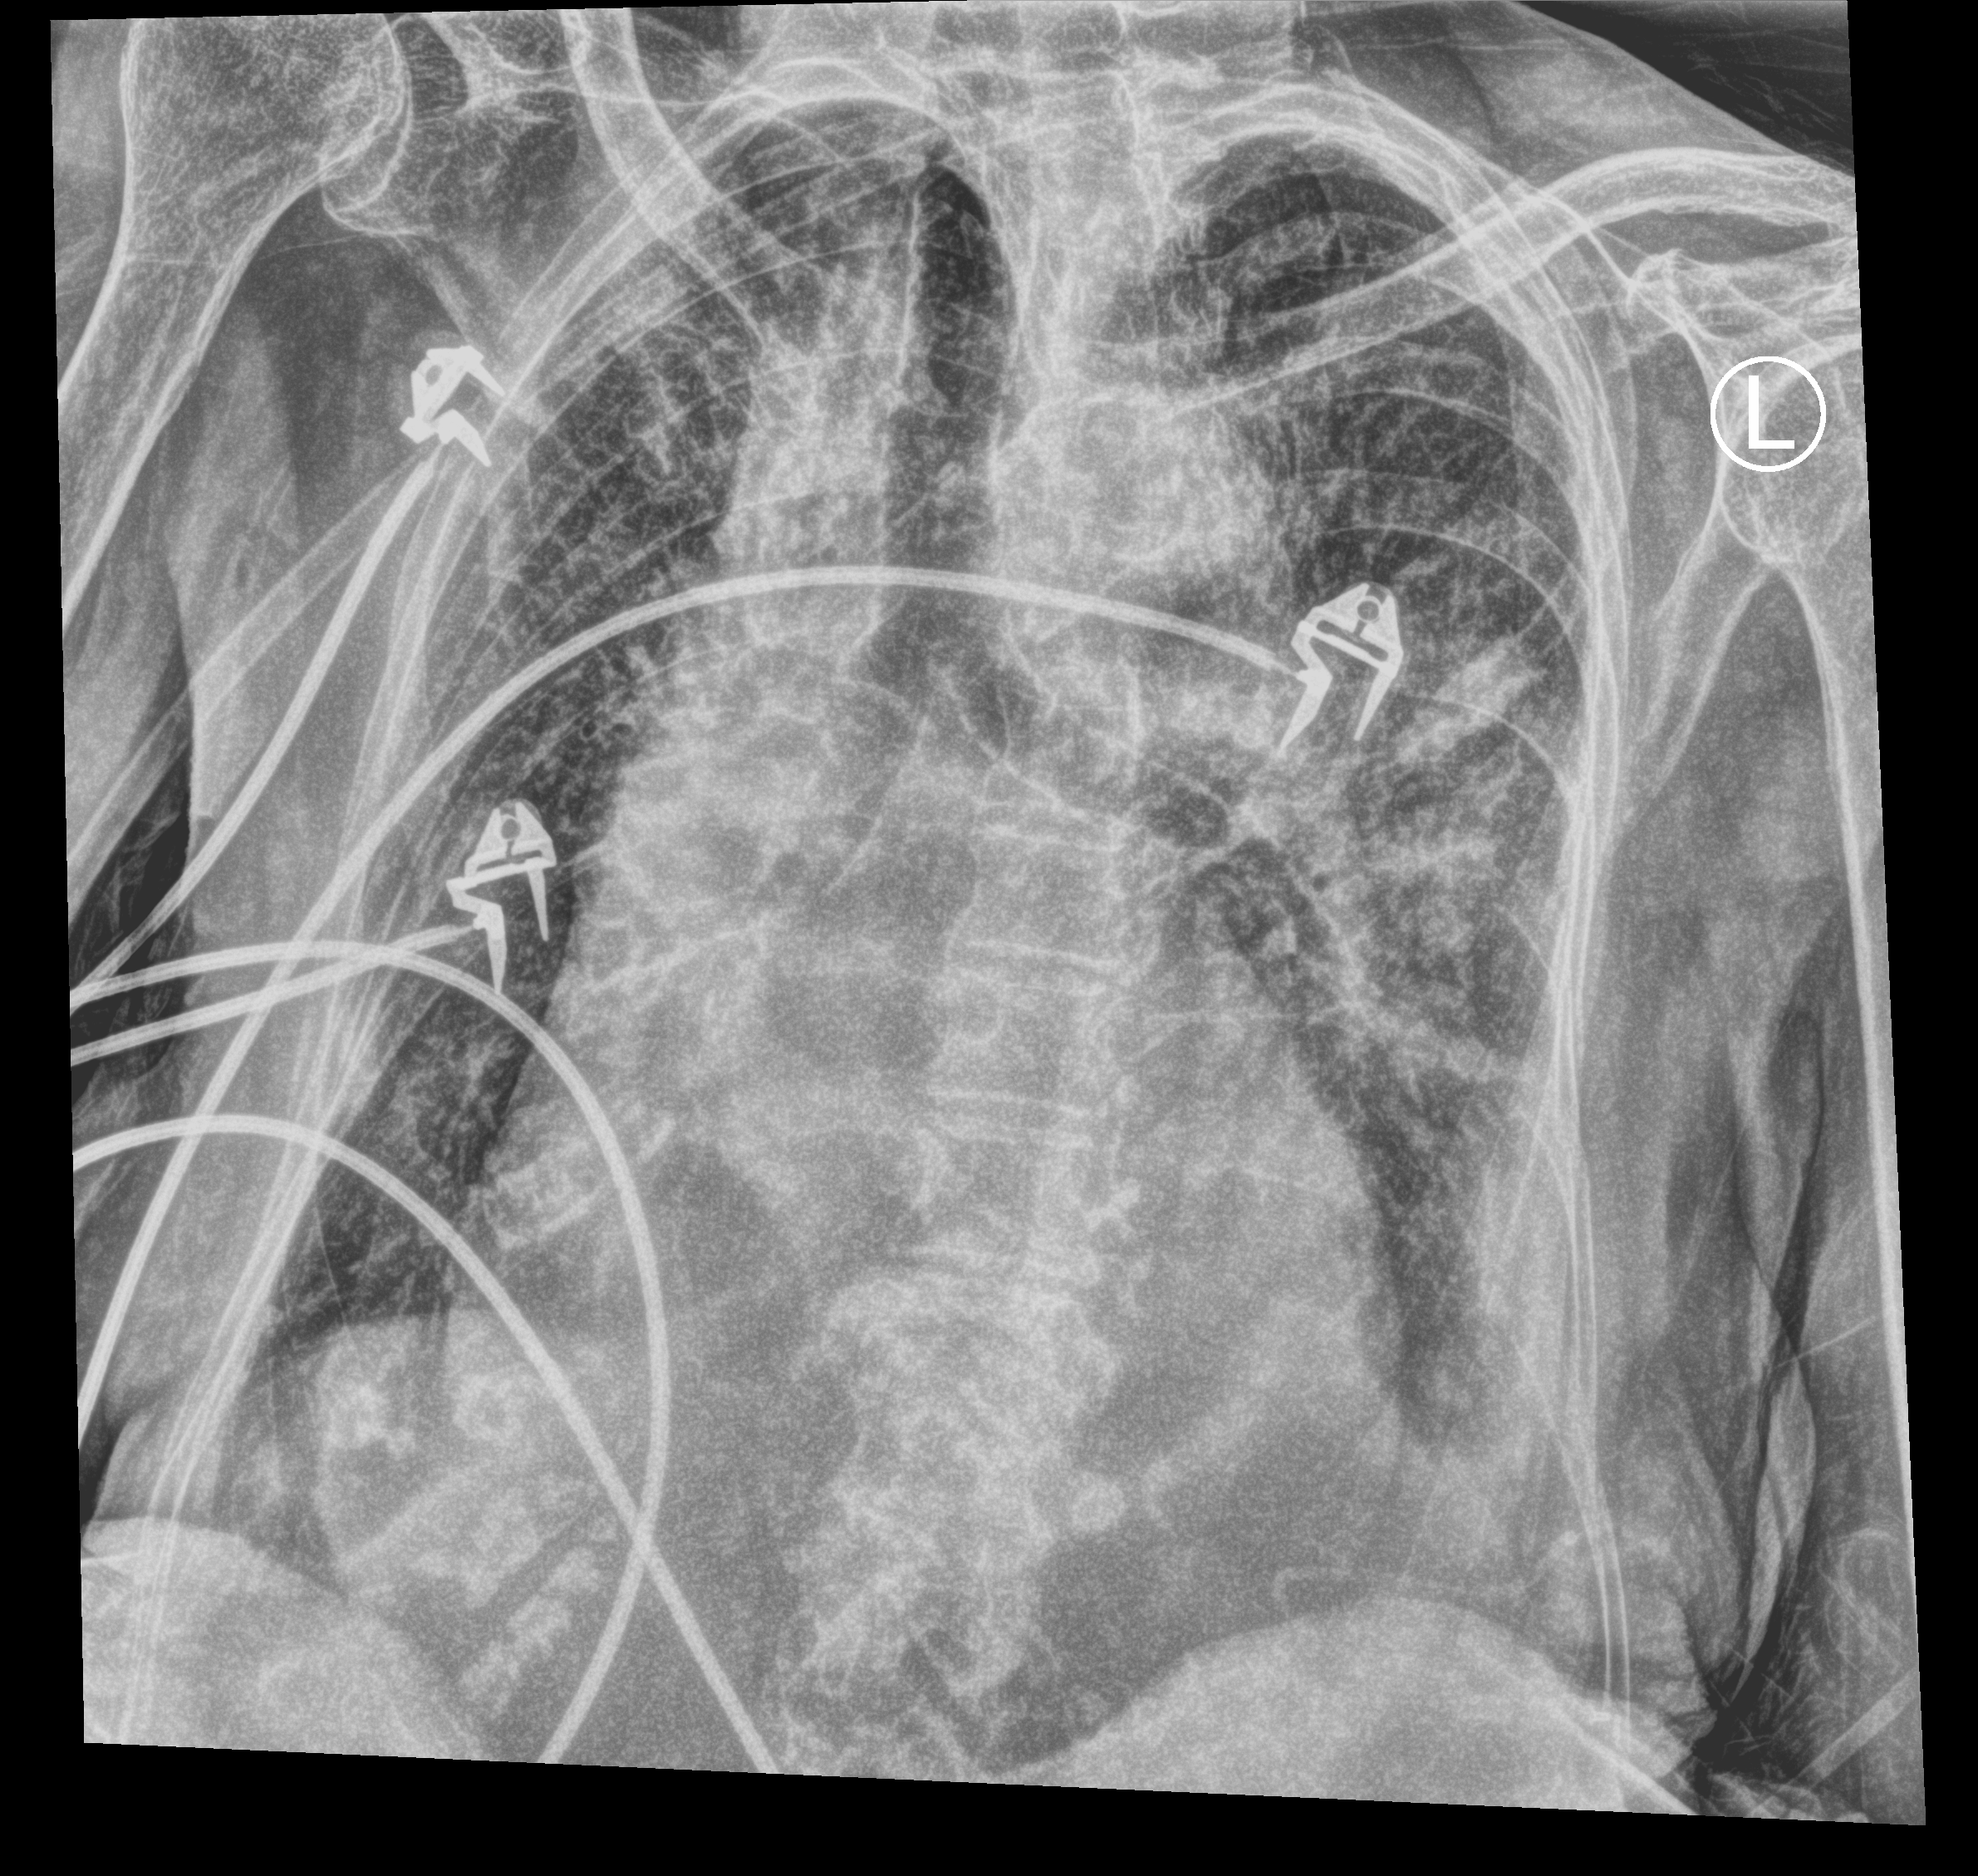
Portable chest radiograph; anteroposterior (AP) projection. Female patient hospitalised with COVID-19, age 75–90 years.
Admission-level facts for this patient (not findings on this image; timing relative to this image not recorded):
- admitted to intensive care during this hospital stay: no
- mechanically ventilated during this hospital stay: no
- length of hospital stay: 8 days